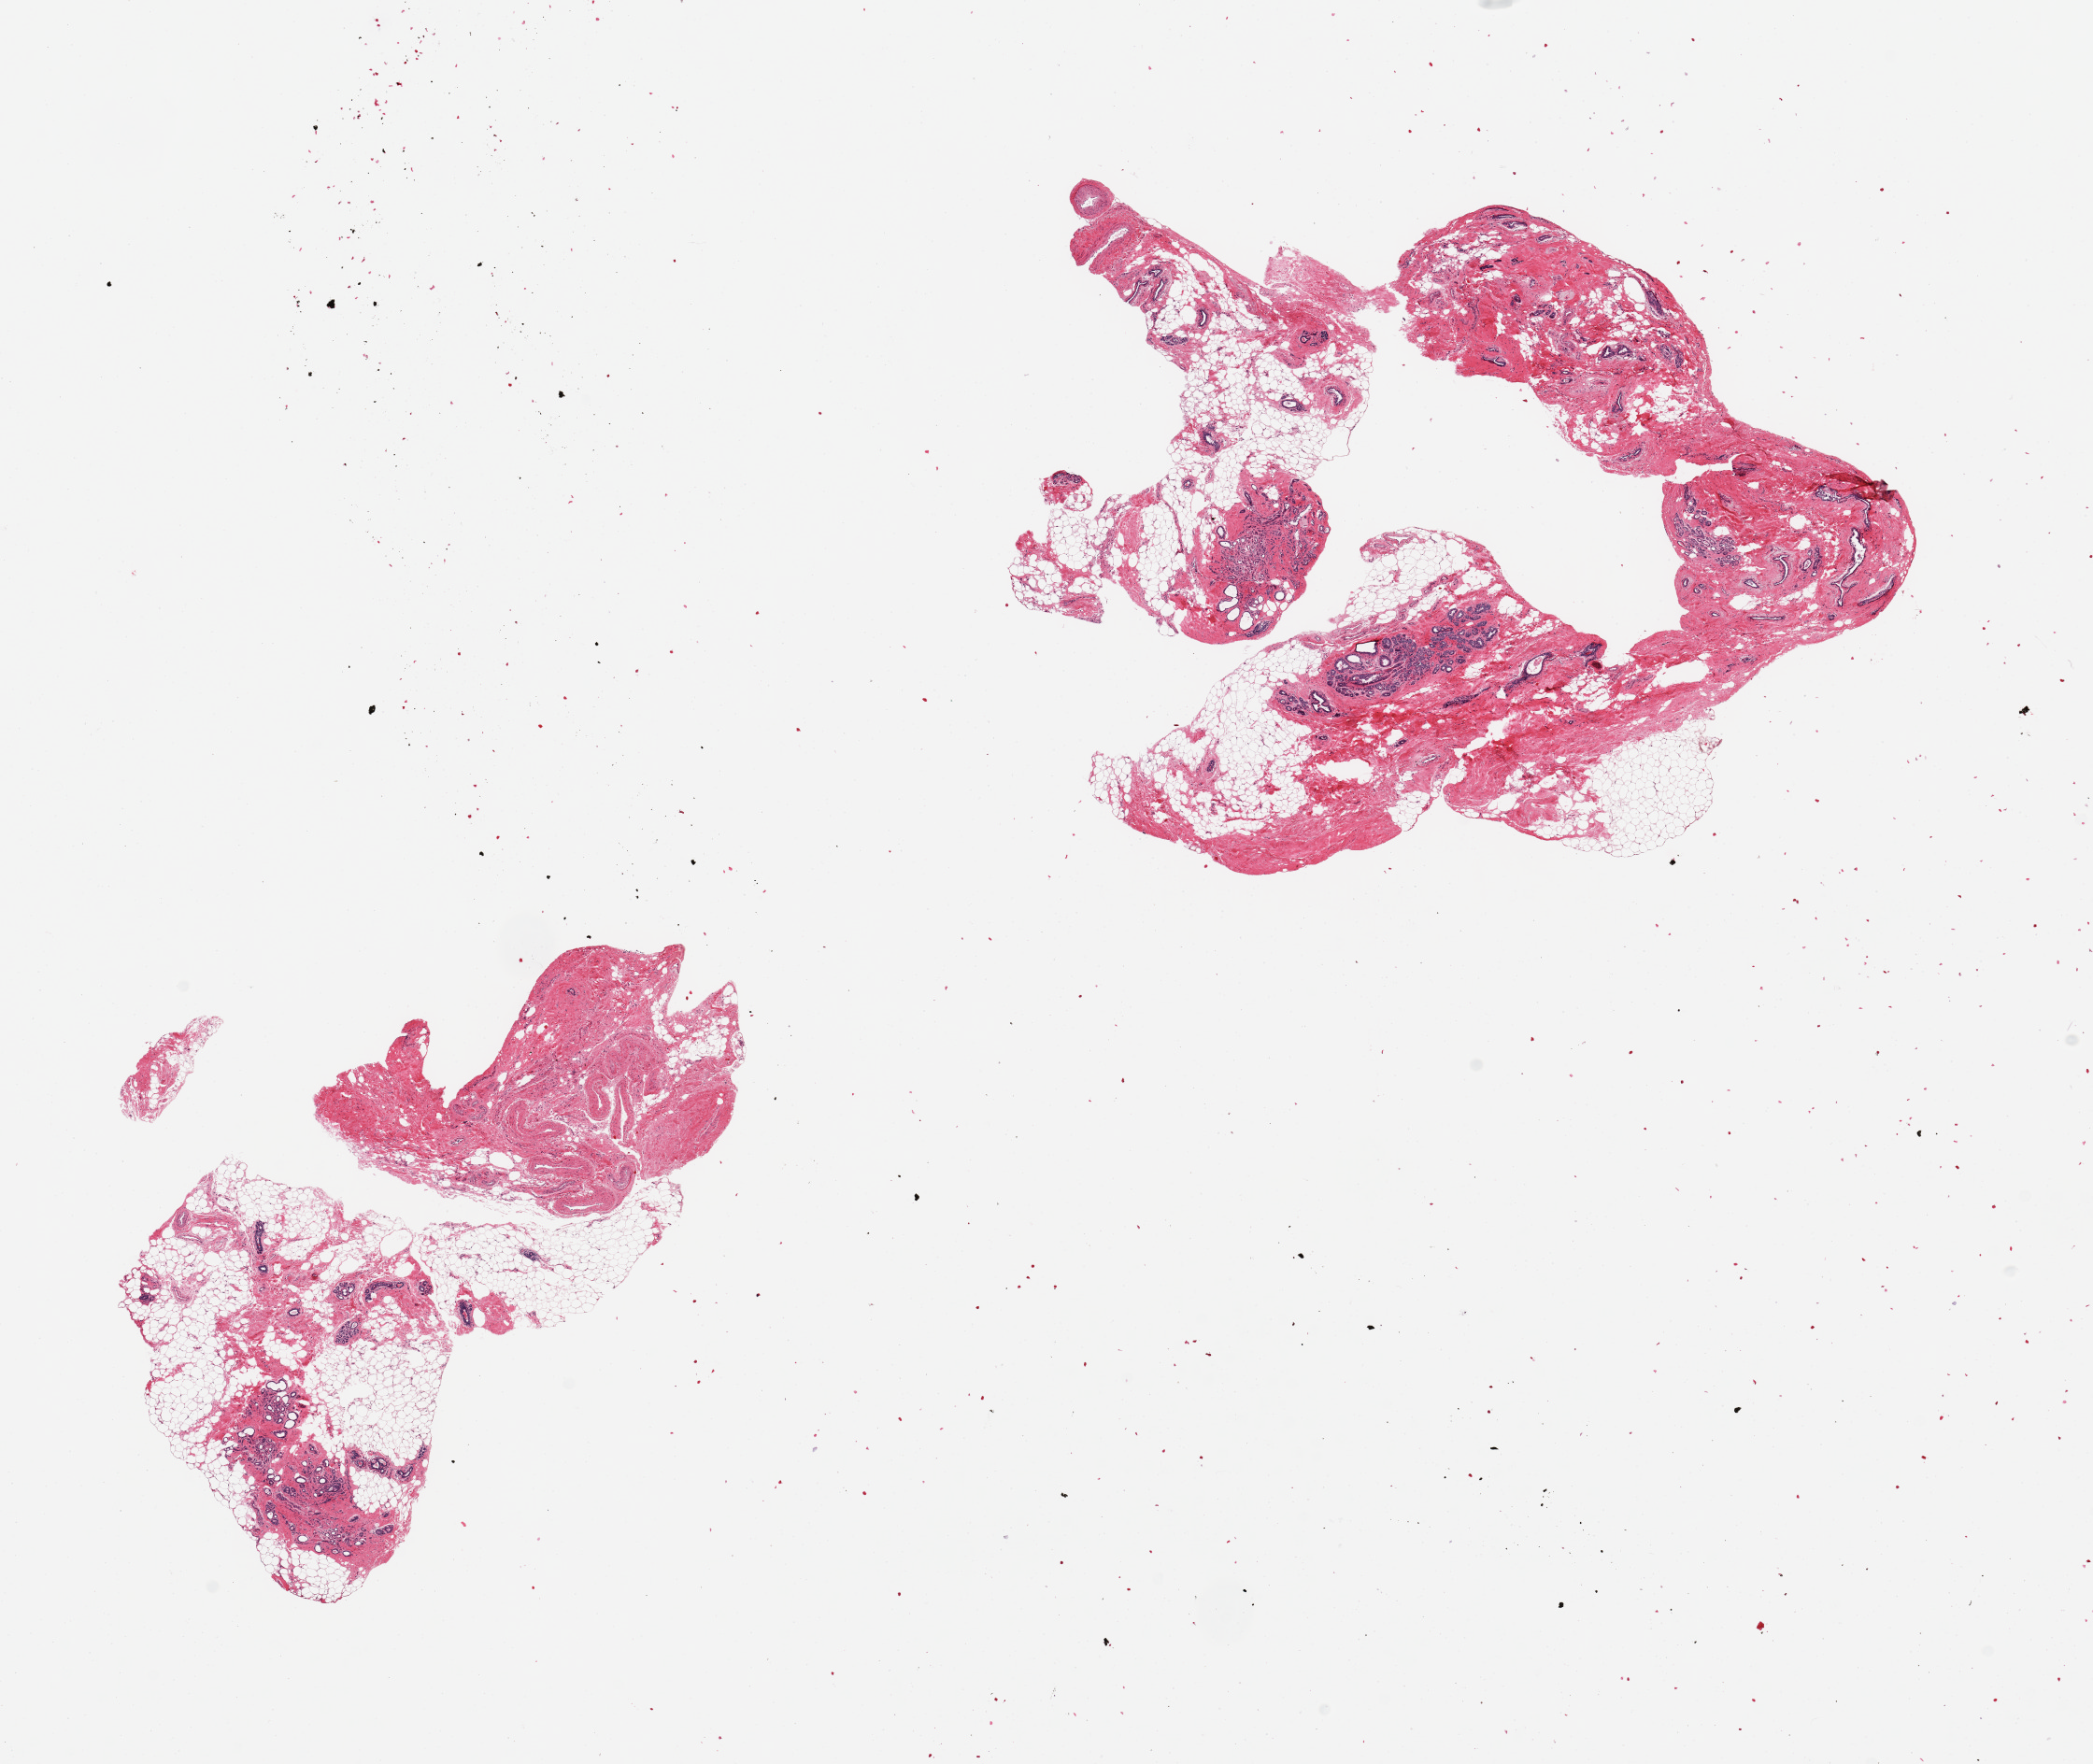
Digitized haematoxylin and eosin-stained section, brightfield, shown as a low-resolution overview of the whole scanned area (about 17.7 x 14.9 mm); PAXgene-fixed paraffin-embedded (PFPE) section; section of breast (target tissue); donor tissue sample.
Pathologist's review note for this sample: 2 pieces, focal sclerosing adenosis; atrophic ductal/lobular elements.